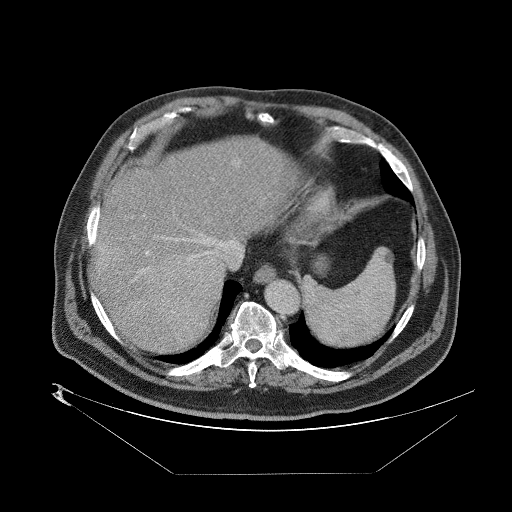
Contrast-enhanced abdominal CT (liver protocol), one axial slice; slice 68 of 89 in the series (ordered by position); one of 2 acquisitions stored at this slice position; soft-tissue window (W 400 / L 40 HU); 2.5 mm slice thickness; 512 × 512 image matrix, field of view 480 × 480 mm. Case-level facts recorded for this patient, not image findings: diagnosis: hepatocellular carcinoma (patient treated with transarterial chemoembolisation; whether this scan precedes or follows treatment is not stated here); TNM stage (as recorded): Stage-II.
Structures marked on this image (semi-automatic segmentation, software-assisted and operator-edited):
- abdominal aorta: box from (x=265, y=281) to (x=299, y=315) px
- liver parenchyma outside the tumour (the mass and vessels are separate outlines, so this box may not span the whole liver): (x=88, y=134)–(x=298, y=350)
- mass: (x=155, y=254)–(x=221, y=316)
- liver vessels: (x=91, y=158)–(x=239, y=316)